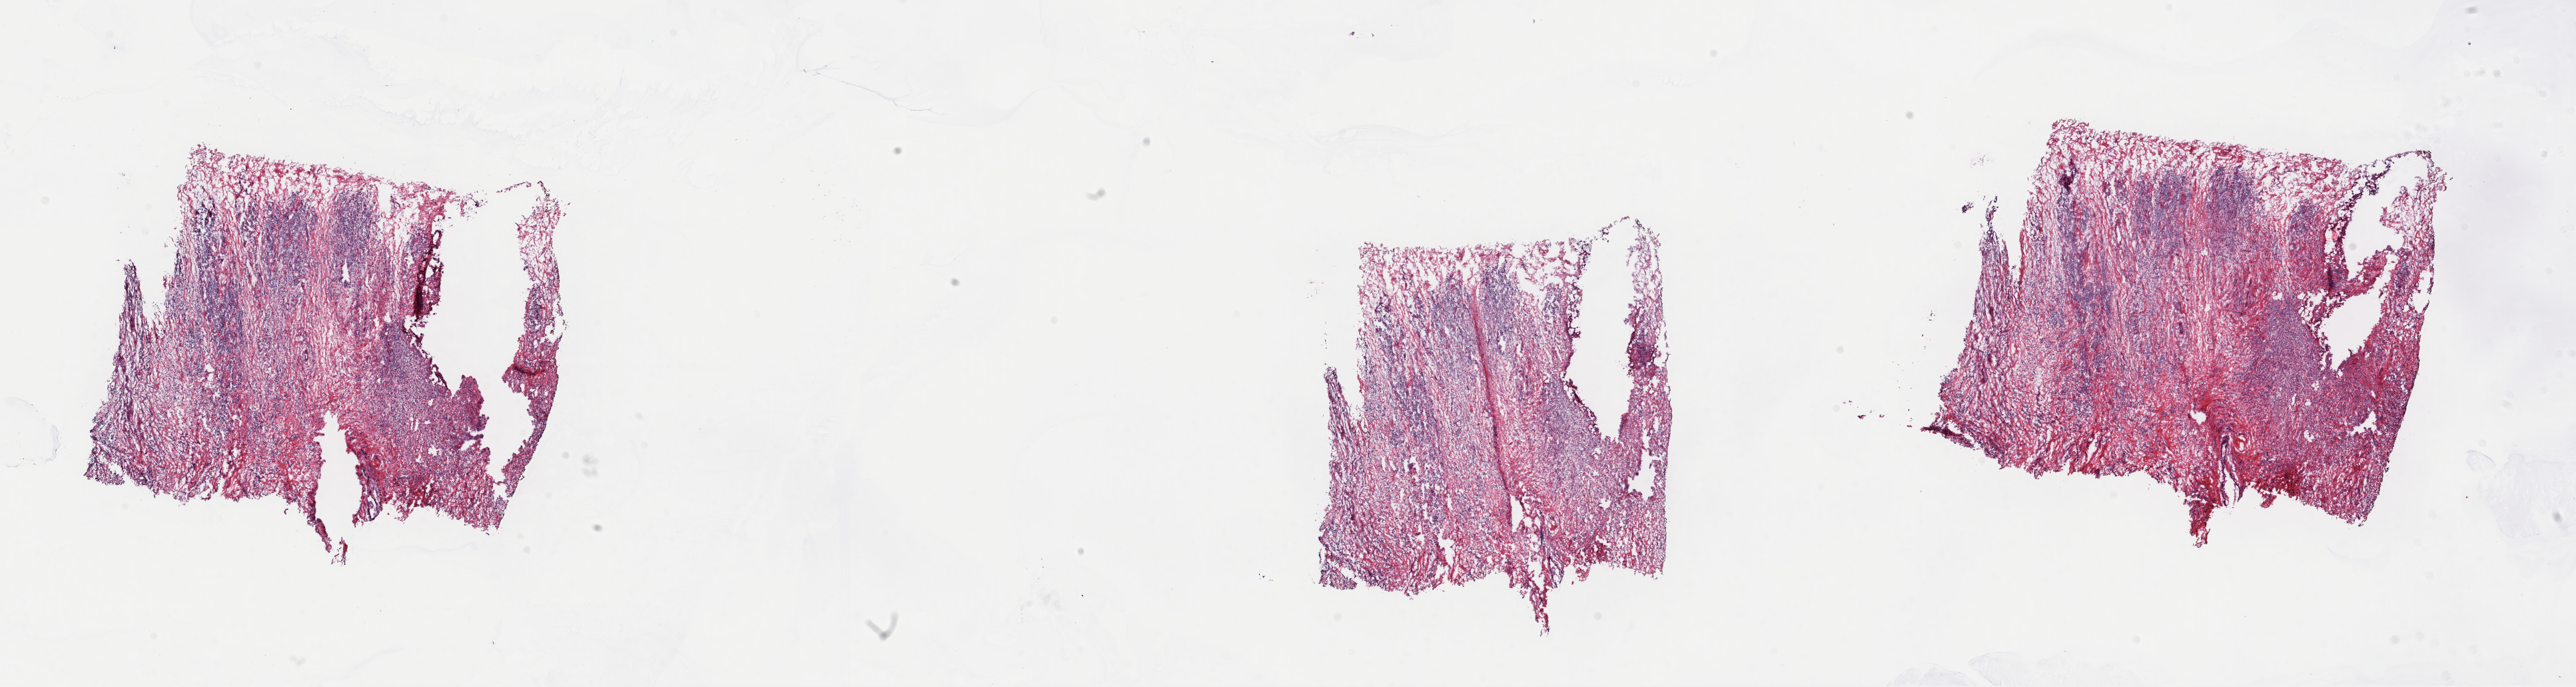
Whole-slide histology image, H&E-stained, a low-resolution overview of the entire scanned area, about 30.5 x 8.1 mm, frozen section from the top of the tissue portion, primary tumour sample from the breast. Female, age 74 years at initial diagnosis. Pathologist review of this section (percent, as recorded): tumour cells 90%, tumour nuclei 80%, normal cells 10%, stromal cells 0%, necrosis 0%. Inflammatory infiltration, as recorded: lymphocyte infiltration 0%, monocyte infiltration 0%, neutrophil infiltration 0%.
Pathologic diagnosis: Lobular carcinoma, NOS. Lymph nodes positive (case pathology): 0 of 8 examined. Laterality: left. AJCC pathologic stage: IIA.